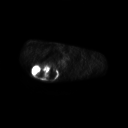
FDG PET of an extremity soft-tissue mass (from a PET/CT study), one axial slice; position 196 of 267 along the scan axis; 3.27 mm slice thickness; 128 × 128 image matrix, field of view 700 × 700 mm. Male patient, age 61 years. Case-level facts recorded for this patient, not image findings: histological type: pleiomorphic spindle cell undifferentiated; grade: high; site of the primary tumour: right parascapusular.
Annotated regions visible in this slice (expert contour drawn on MRI and transferred to this co-registered scan by the dataset authors):
- gross tumour volume including surrounding oedema: box from (x=31, y=64) to (x=60, y=79) px
- gross tumour volume (mass): (x=31, y=64)–(x=58, y=78)